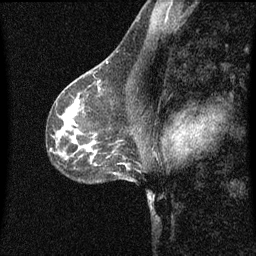
Breast MRI (dynamic contrast-enhanced), one sagittal slice; position 39 of 60 along the scan axis; dynamic contrast-enhanced series, image 2 of 3 at this slice position (ordered by acquisition); 1.5 T; TE 4.2 ms, TR 8.4 ms; 256 × 256 image matrix, field of view 200 × 200 mm. Patient: female, 41 years.
Annotated regions visible in this slice (semi-automatic segmentation, software-assisted and operator-edited):
- analysis volume of interest (the breast-tissue region the enhancement analysis was run in; not a lesion): bounding box <94,72,119,97> (left, top, right, bottom; pixels)
- tumour enhancement mask (voxels above the 70 % enhancement threshold inside the analysis volume of interest): <94,72,101,89>